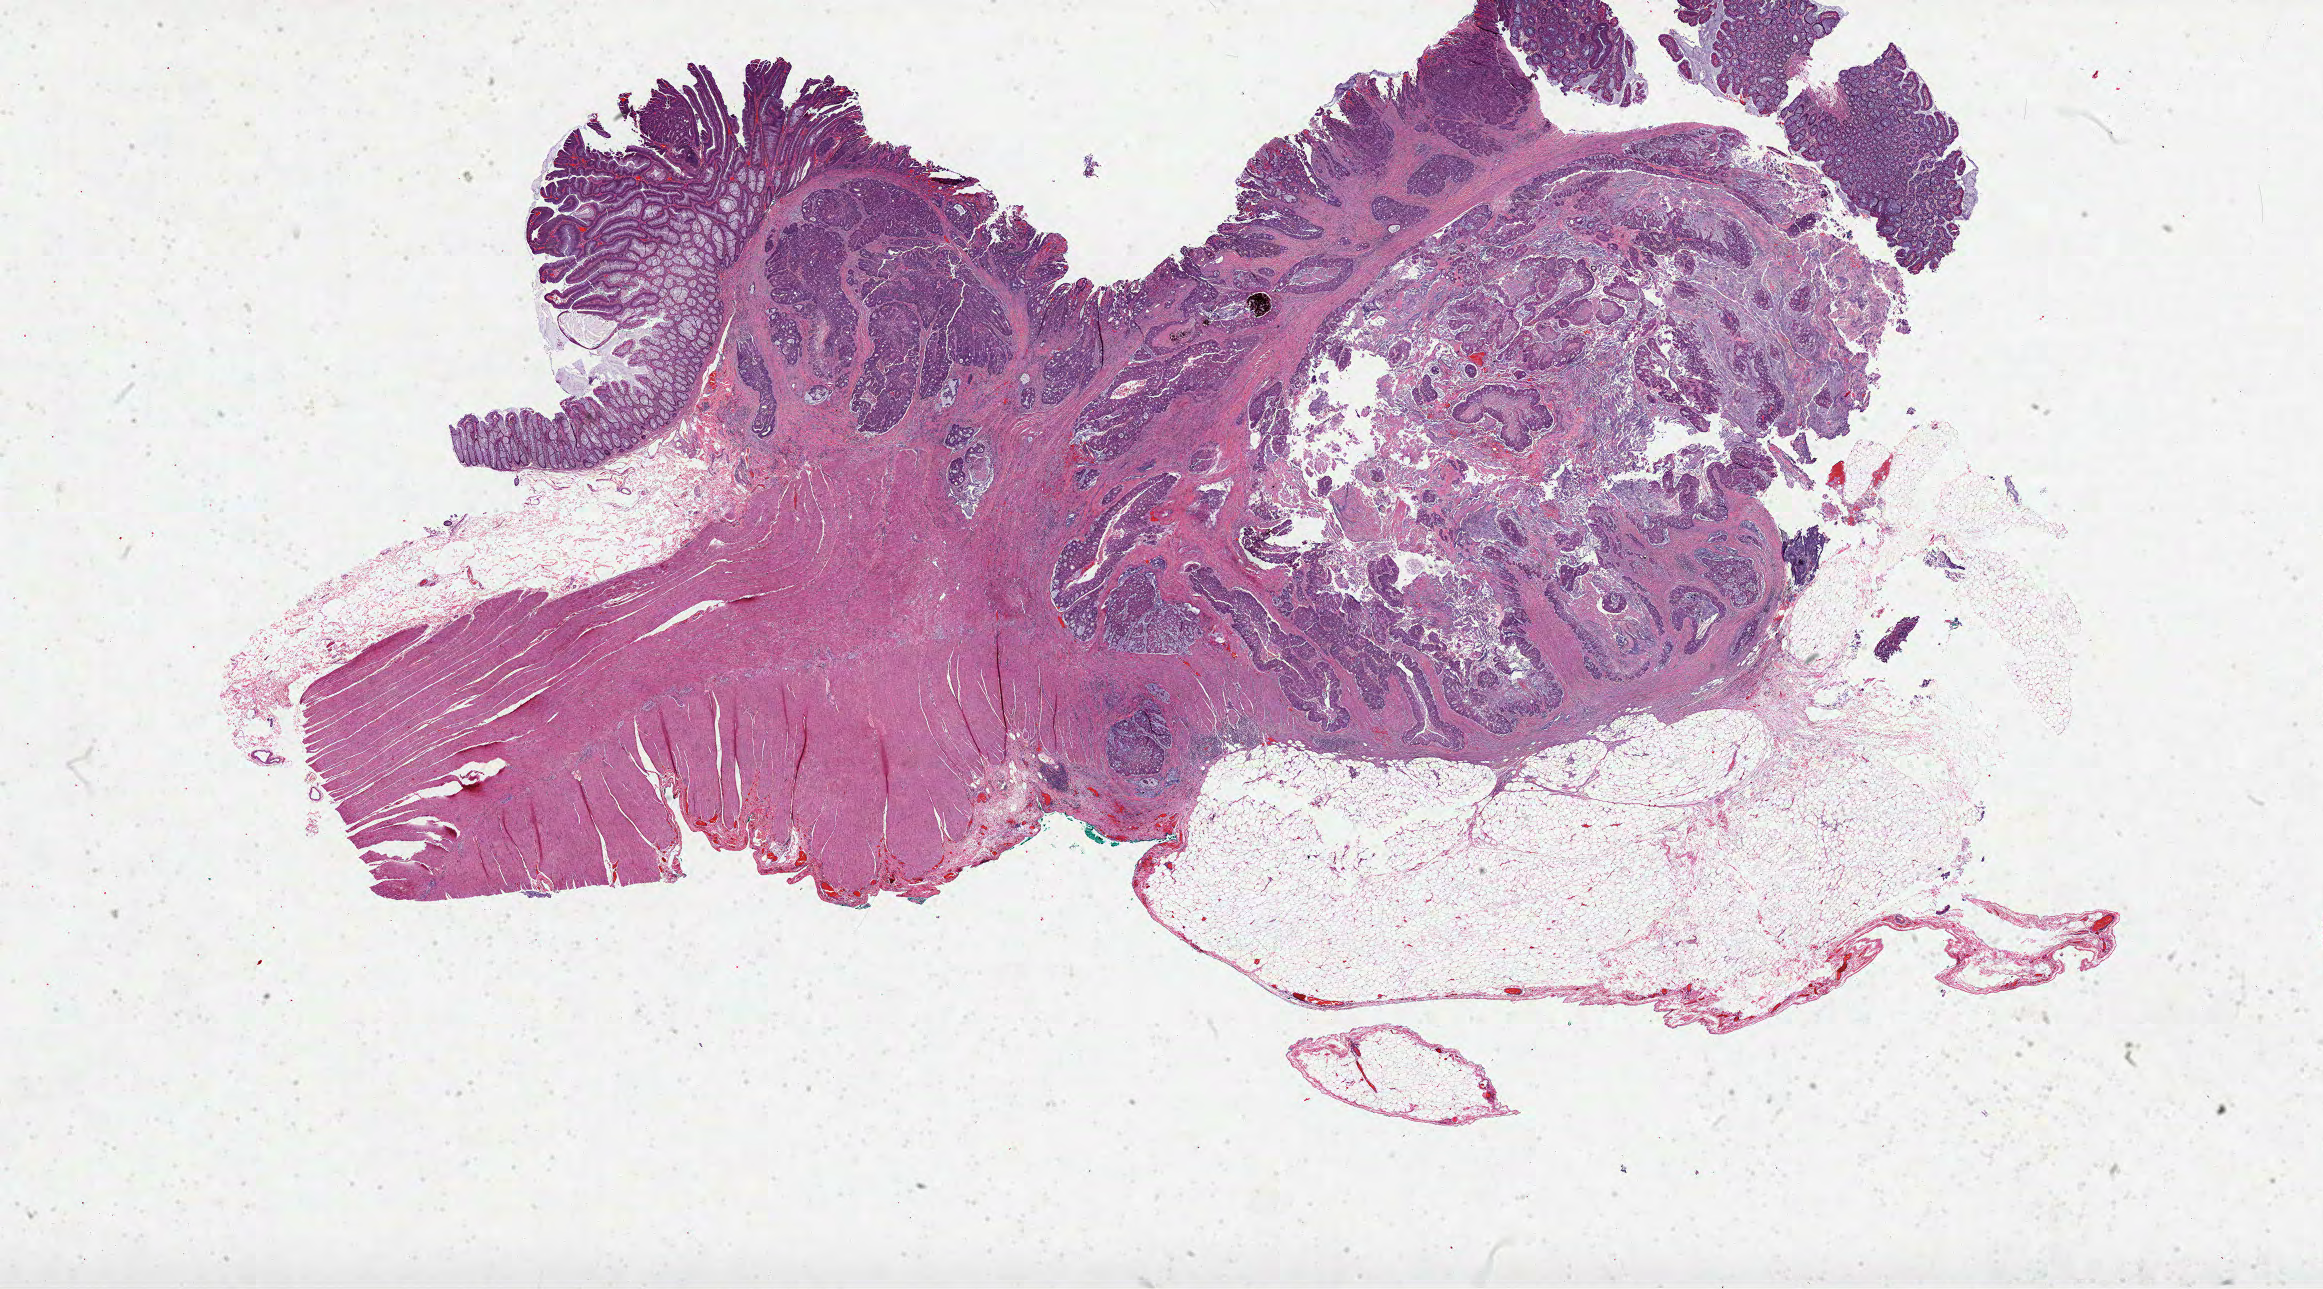
Digitized H&E-stained tissue section (whole slide) — shown as a low-resolution overview of the whole scanned area (about 37.5 x 20.8 mm, from a 40x scan), formalin-fixed paraffin-embedded (FFPE) diagnostic section, colon, primary tumour sample. Patient: male, age at initial diagnosis 74 years.
Diagnosis: Adenocarcinoma, NOS. AJCC pathologic stage: IIA (7th edition).